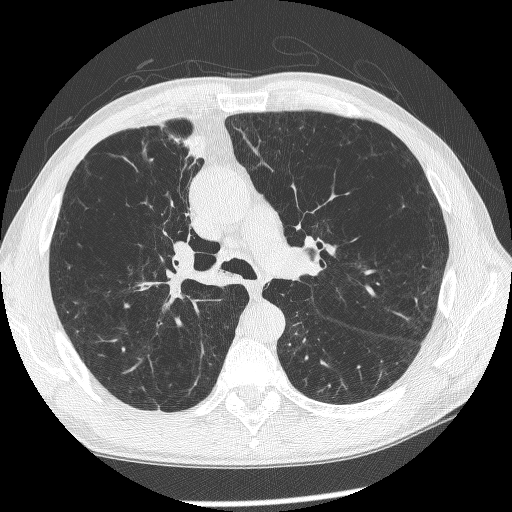
Axial slice from a low-dose chest CT screening exam. First (baseline) screen. Lung window (W 1500 / L -600 HU). 1.25 mm slice thickness. Lung (sharp) reconstruction kernel (BONE). 120 kVp. Slice 158 of 266 in the series. 512 × 512 image matrix. Male, age 60 years at enrolment. Current smoker at enrolment.
Lesion marked by an expert reader, bounding box (x1, y1, x2, y2) in pixels: (144, 209, 225, 301). Screening reader's record for this exam (one nodule recorded; not confirmed to be the boxed lesion): non-calcified nodule or mass ≥4 mm, right upper lobe, 12 × 8 mm, spiculated (stellate) margins, mixed attenuation. Later outcome: lung cancer diagnosed 208 days after this screen — squamous cell carcinoma, NOS, right upper lobe, right middle lobe, right main stem bronchus, poorly differentiated (G3), stage IV (AJCC 6th edition).